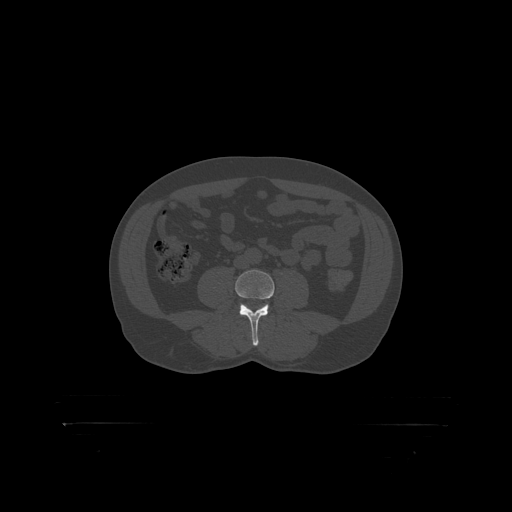
CT including the spine, one axial slice; slice 233 of 399 in the series (ordered by position); reconstruction kernel STANDARD; bone window (W 1800 / L 400 HU); 1.25 mm slice thickness; 512 × 512 image matrix, field of view 650 × 650 mm. Male patient, age 46 years. From the clinical record (not read from this slice): primary cancer: skin.
Structures marked on this image (semi-automatic segmentation, software-assisted and operator-edited):
- L4 vertebra: bounding box [x1, y1, x2, y2] px = [236, 270, 275, 319]